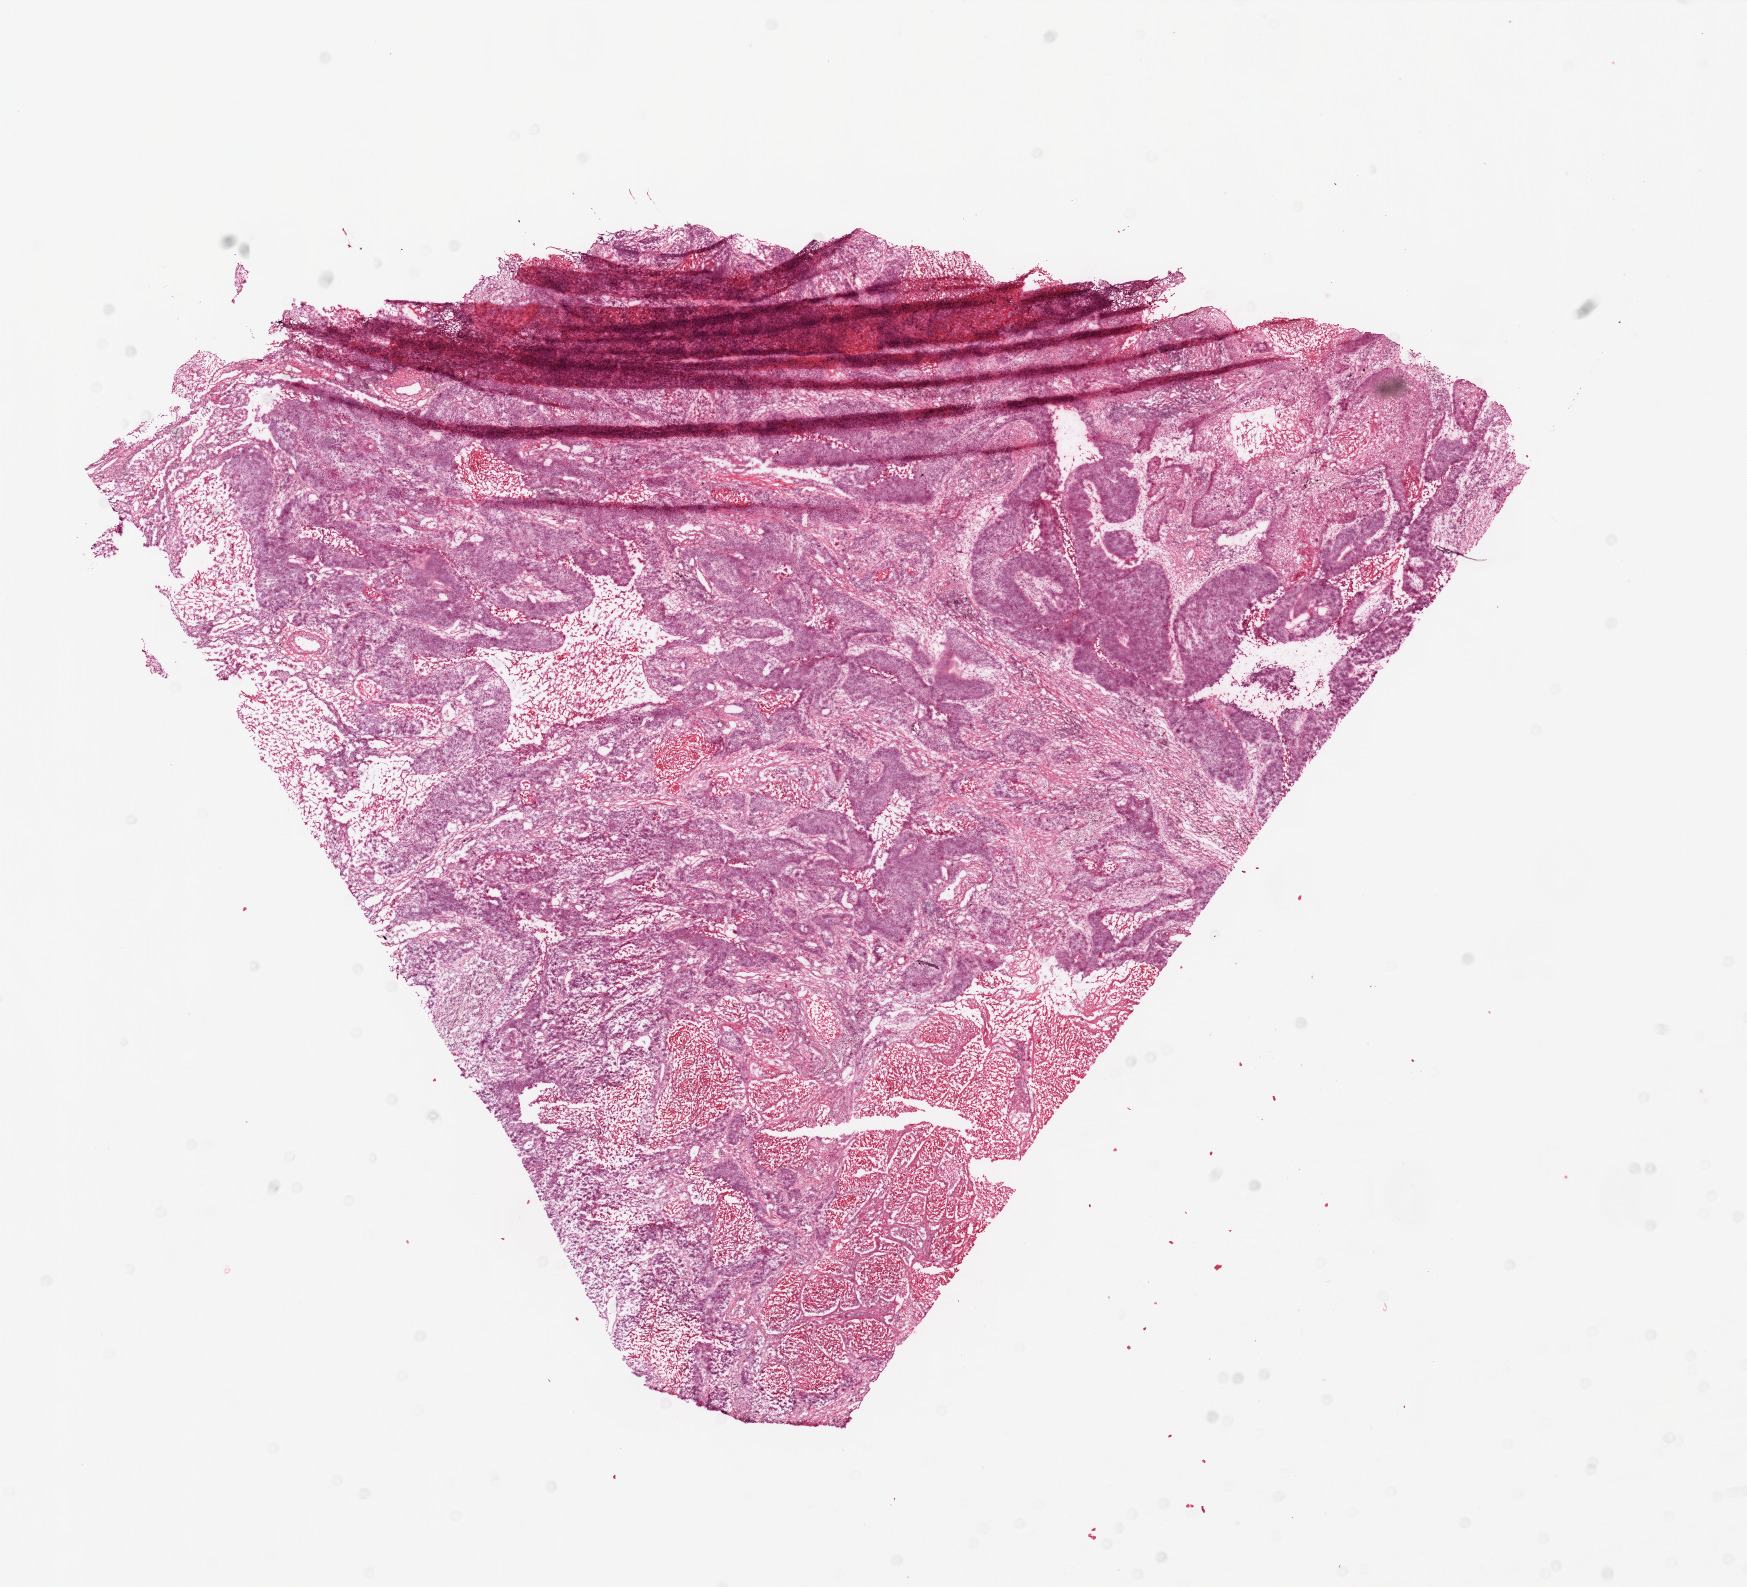
Whole-slide histology image, Hematoxylin and eosin (H&E) stained — a low-resolution overview of the entire scanned area, about 14.0 x 12.7 mm; frozen section from the top of the tissue portion; primary tumour sample from the lung. Male patient; age at initial diagnosis 61 years. Composition of this section per pathologist review: tumour nuclei 60%, necrosis 5%.
* laterality: left
* histologic diagnosis: Squamous cell carcinoma, NOS
* AJCC pathologic stage: IB